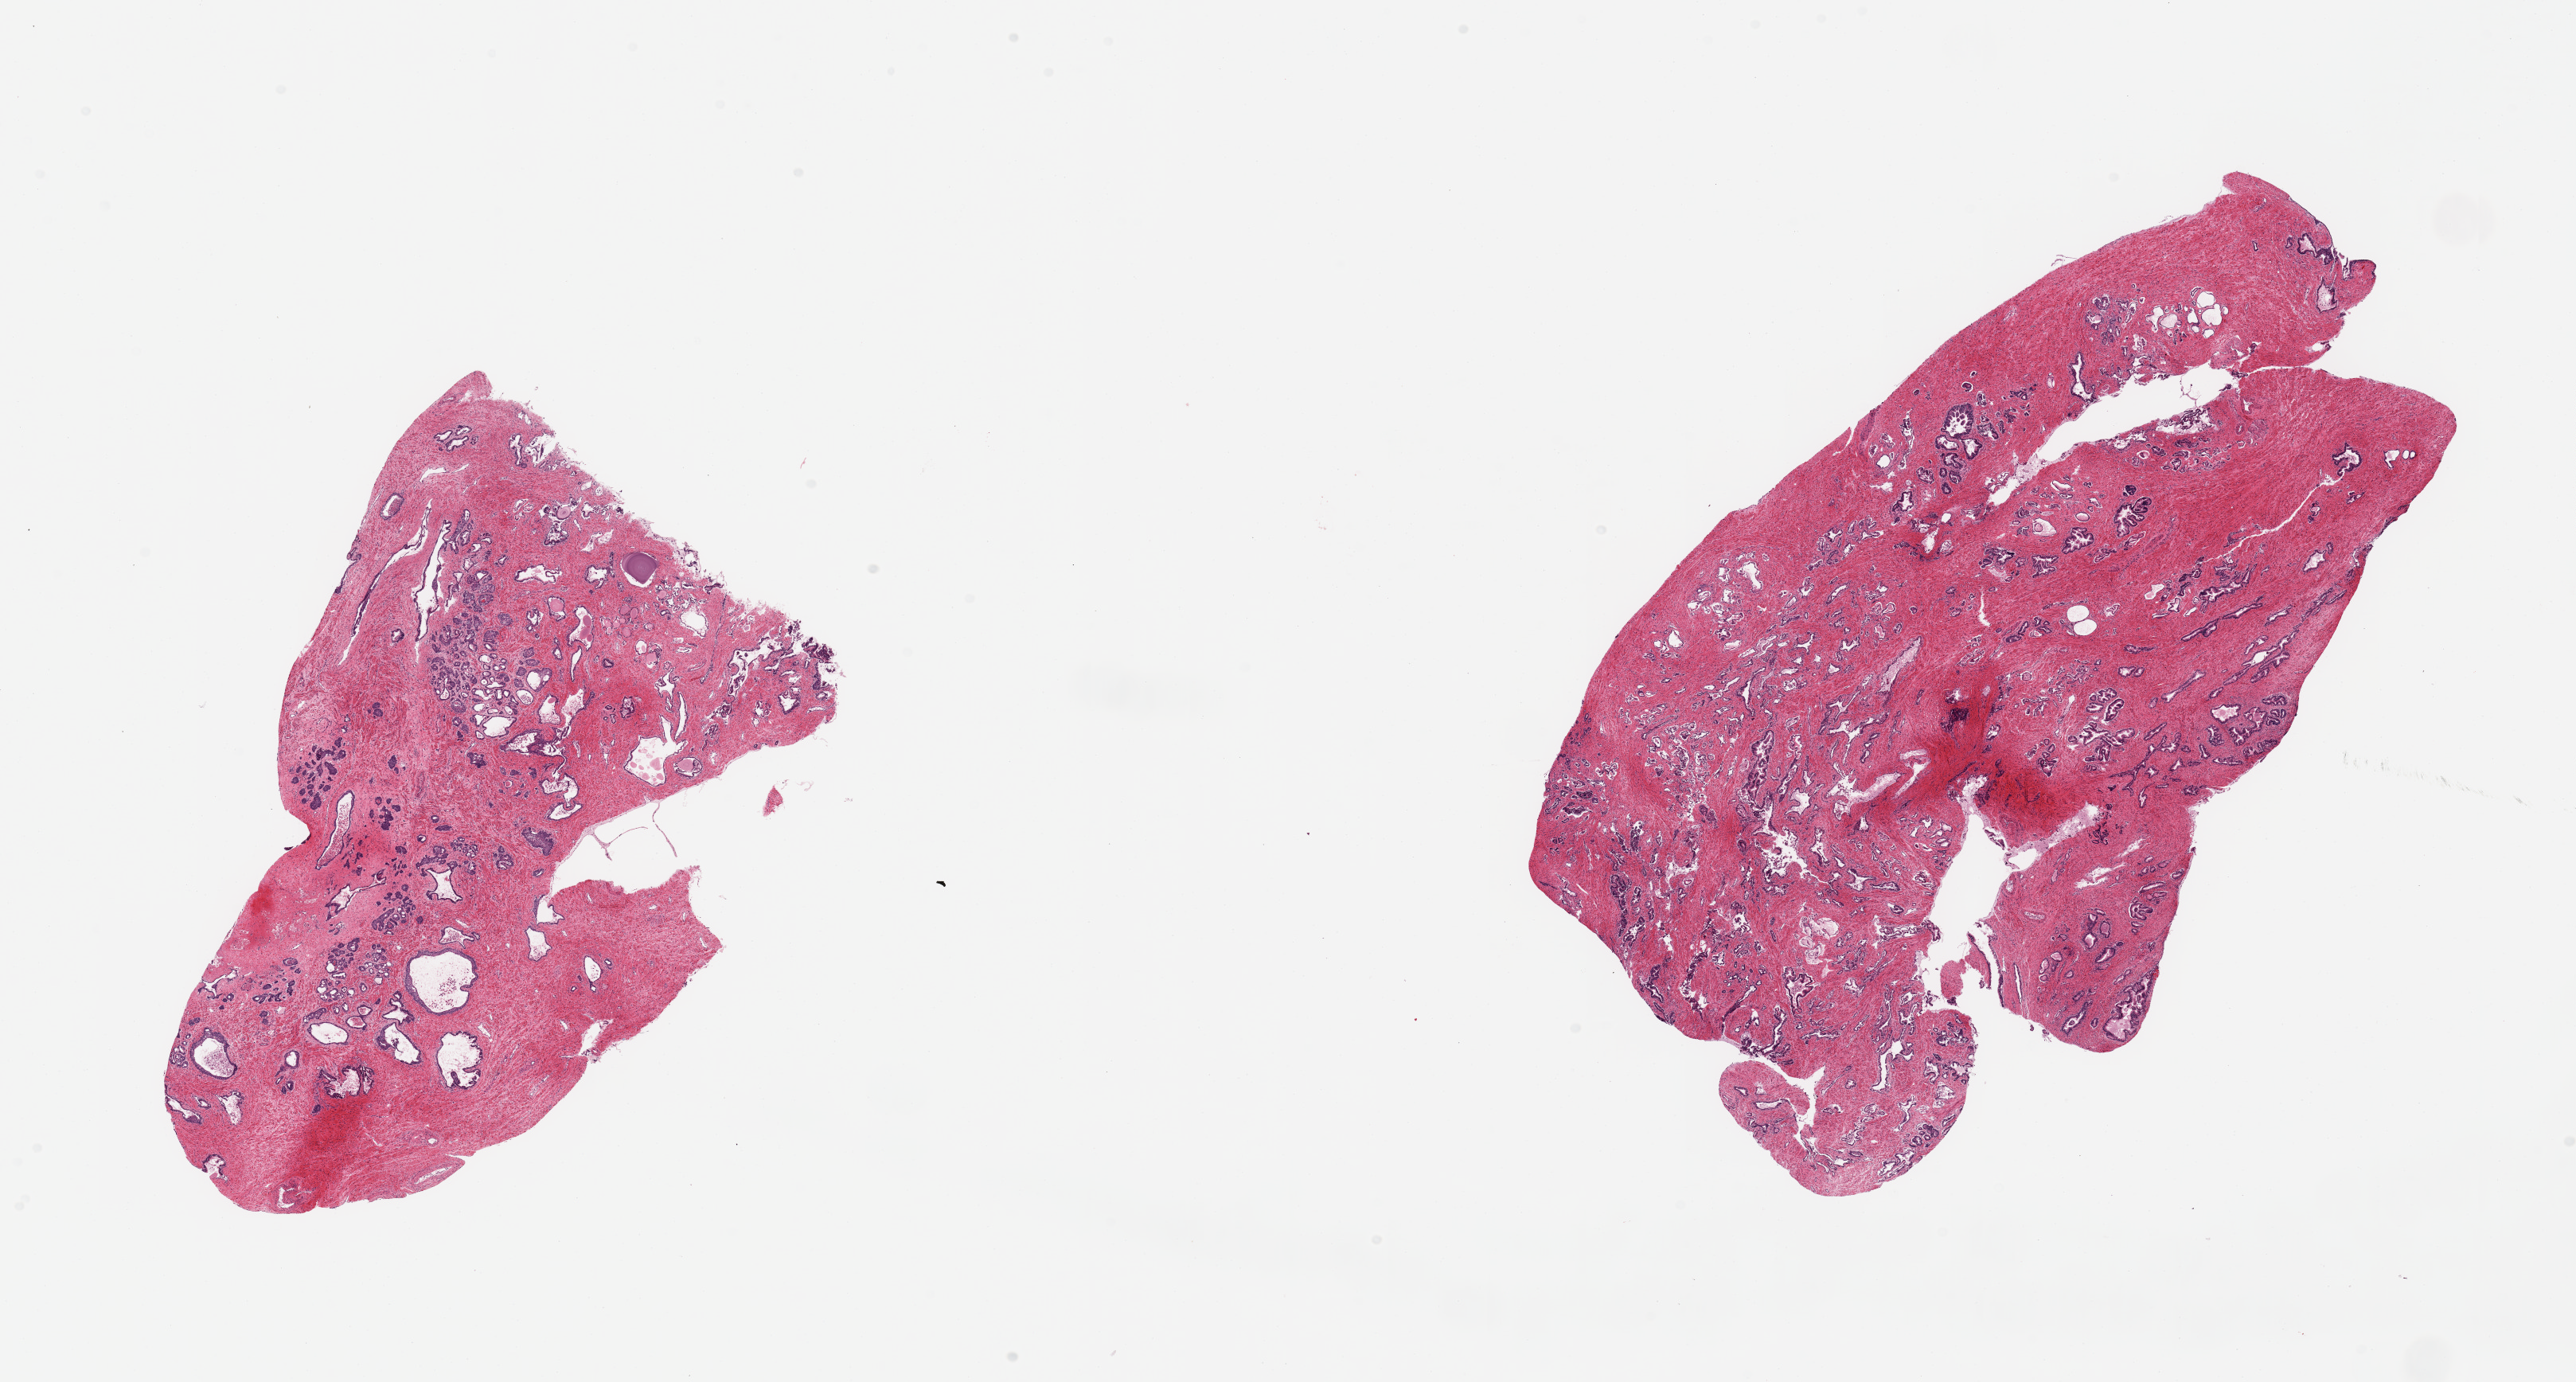
Whole-slide image, H&E stain — shown as a low-resolution overview of the whole scanned area (about 25.6 x 13.7 mm), PAXgene-fixed paraffin-embedded (PFPE) section, section of prostate (target tissue), tissue donor sample. Male donor.
Reviewer comment on this tissue sample: 2 pieces; 1 piece contains a 5.4 mm by 2.6 mm area of atypical glands with prominent nucleoli and an infiltrative pattern diagnostic of carcinoma; Gleason grading is 3+4=7. The other piece has a similar area 1.9x1.5mm. Affected areas are marked on the images.